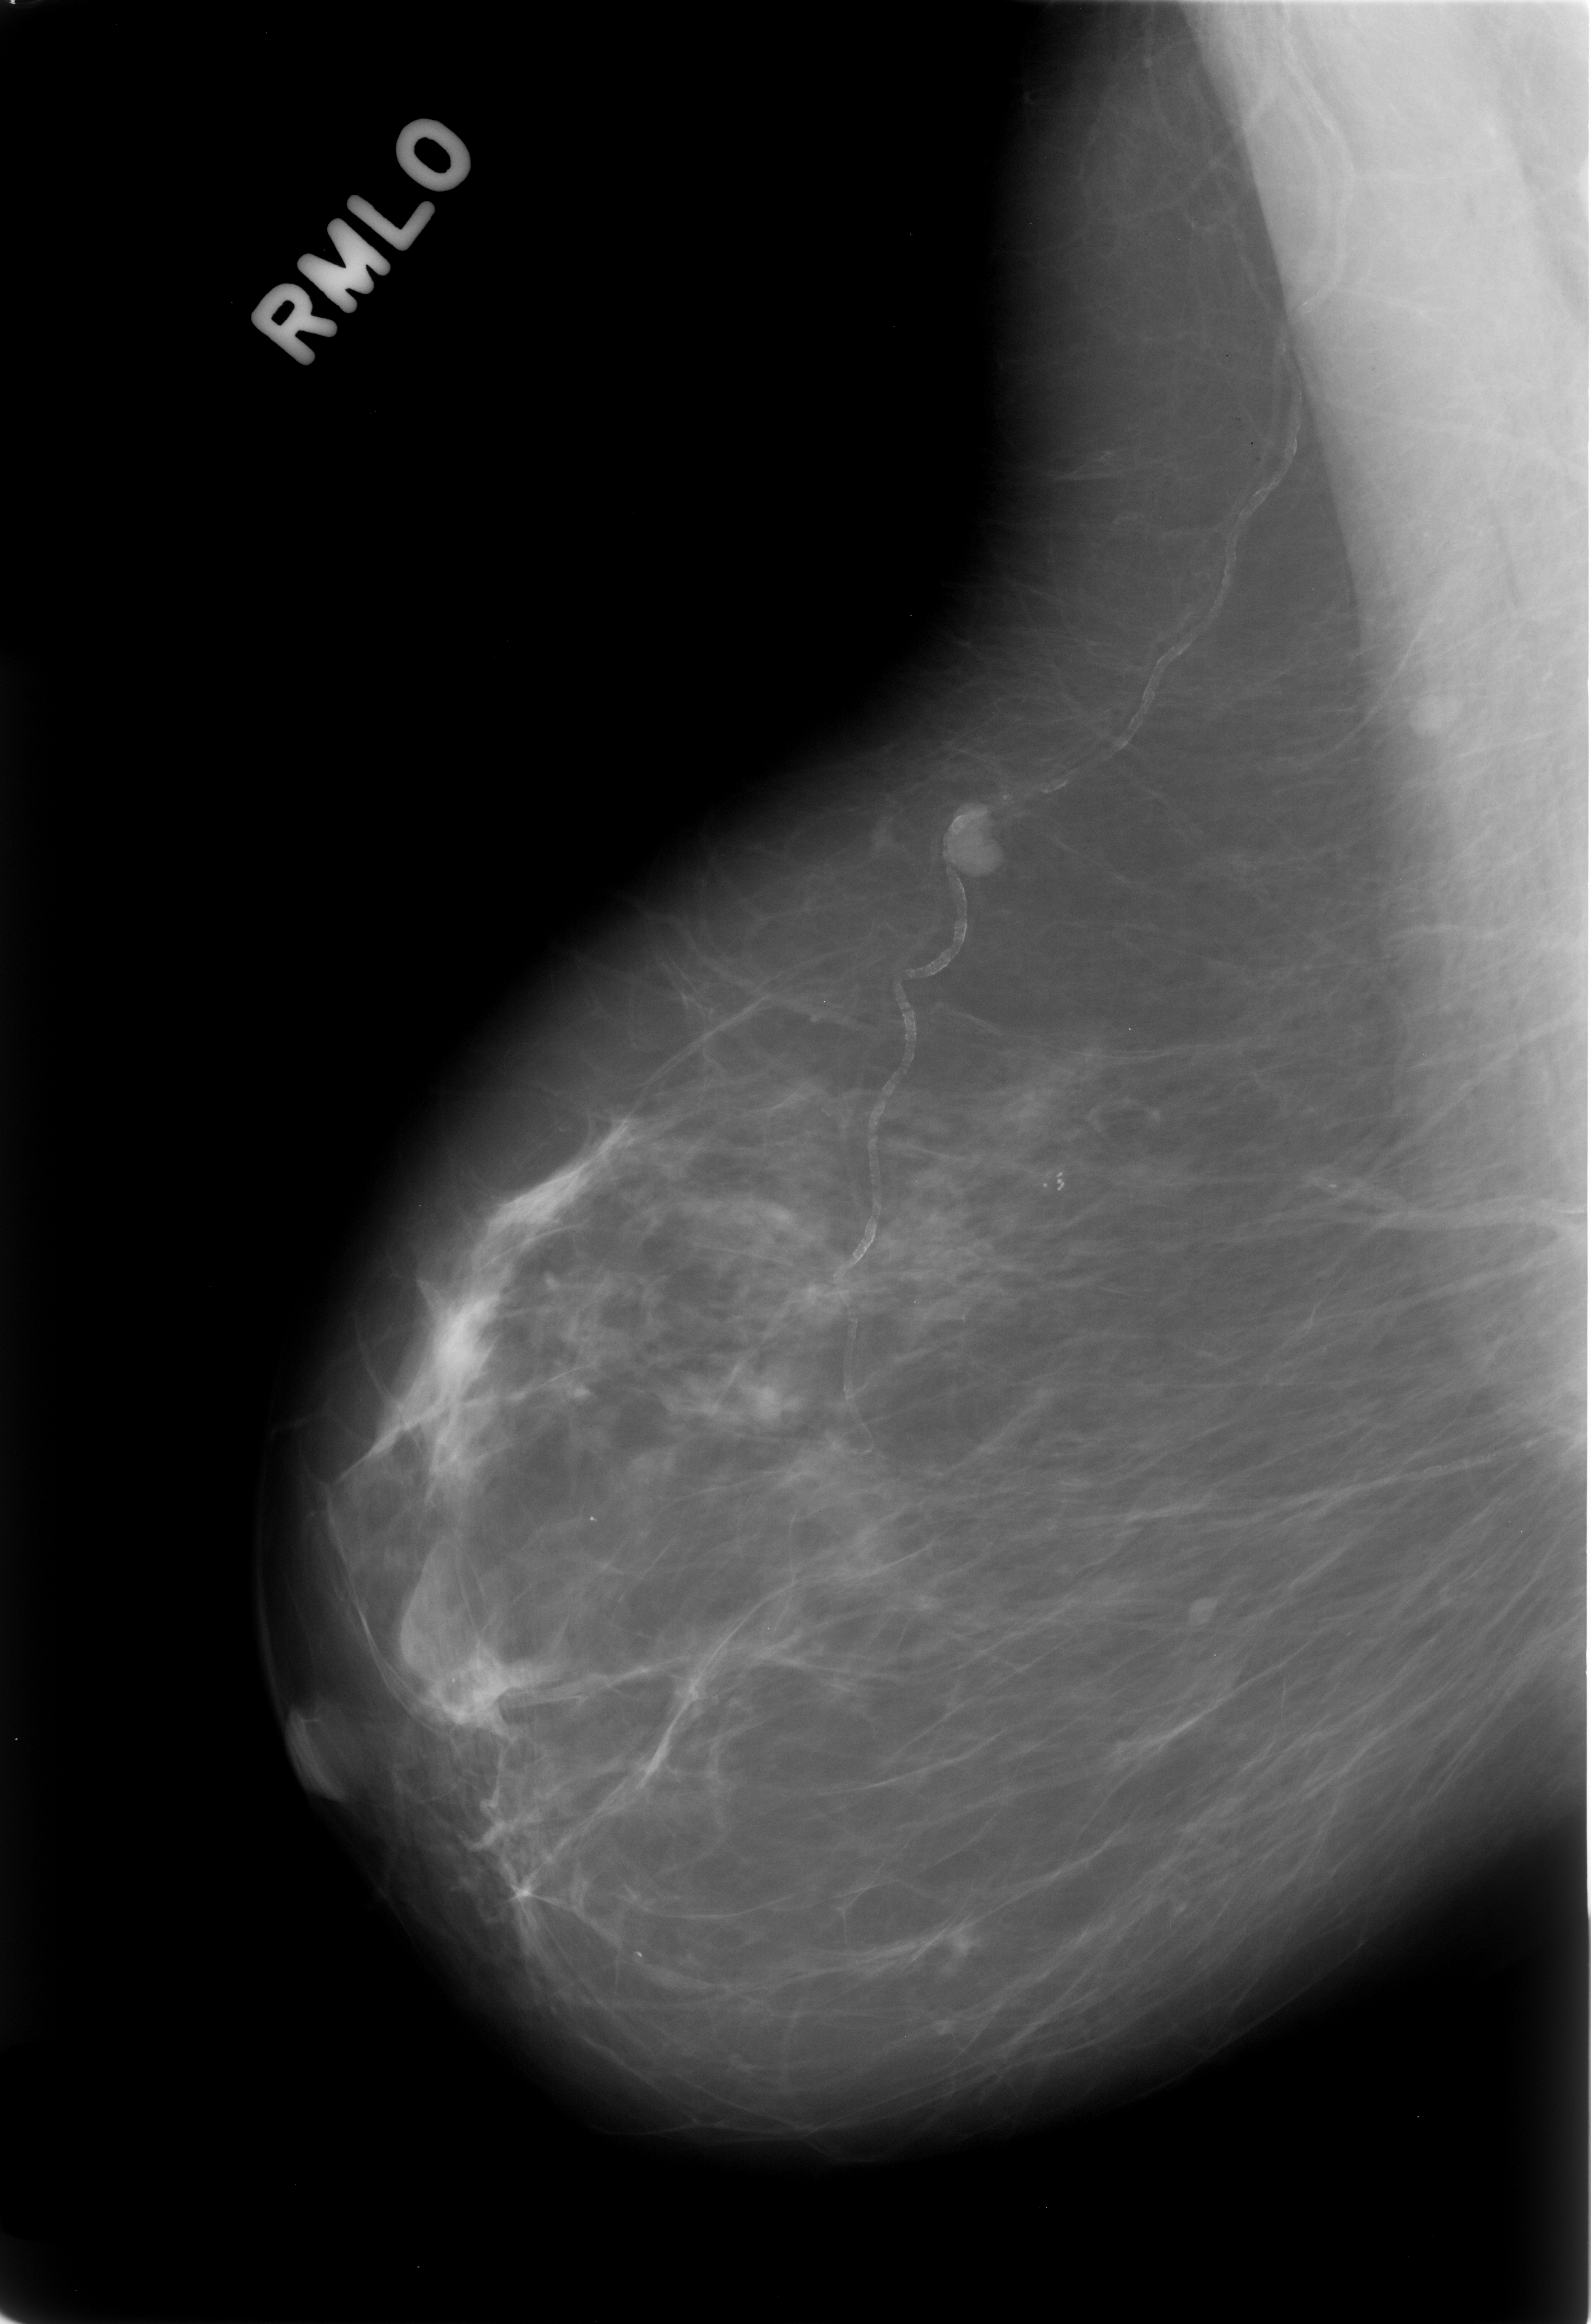
Mammogram (digitized film); right breast; MLO view; breast composition: almost entirely fatty (BI-RADS density category 1 of 4).
- Marked findings (only marked abnormalities are described; nothing is implied about the rest of the image): mass, shape lobulated, margins circumscribed; BI-RADS assessment category 3; pathology (as recorded): benign.